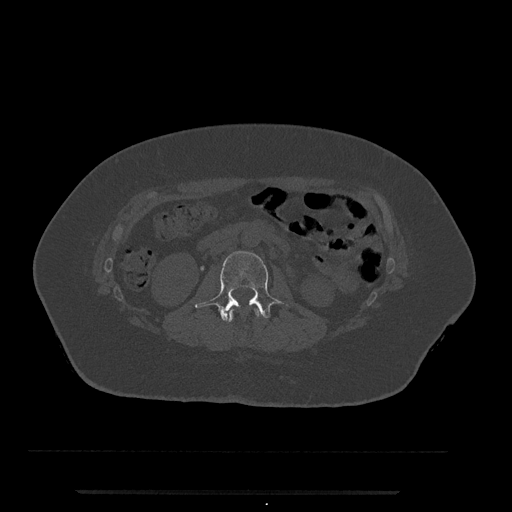
CT including the spine, one axial slice. Position 43 of 797 along the scan axis. Reconstruction kernel Br40s/3. Bone window (W 1800 / L 400 HU). 512 × 512 image matrix, field of view 440 × 440 mm. Female patient, age 51 years. From the clinical record (not read from this slice): primary cancer: neuro; vertebrae with lytic lesions (as recorded): T8.
Outlined on this slice (semi-automatically segmented with operator editing):
- L1 vertebra: bounding box [x1, y1, x2, y2] px = [227, 308, 262, 322]
- L2 vertebra: [195, 251, 289, 321]